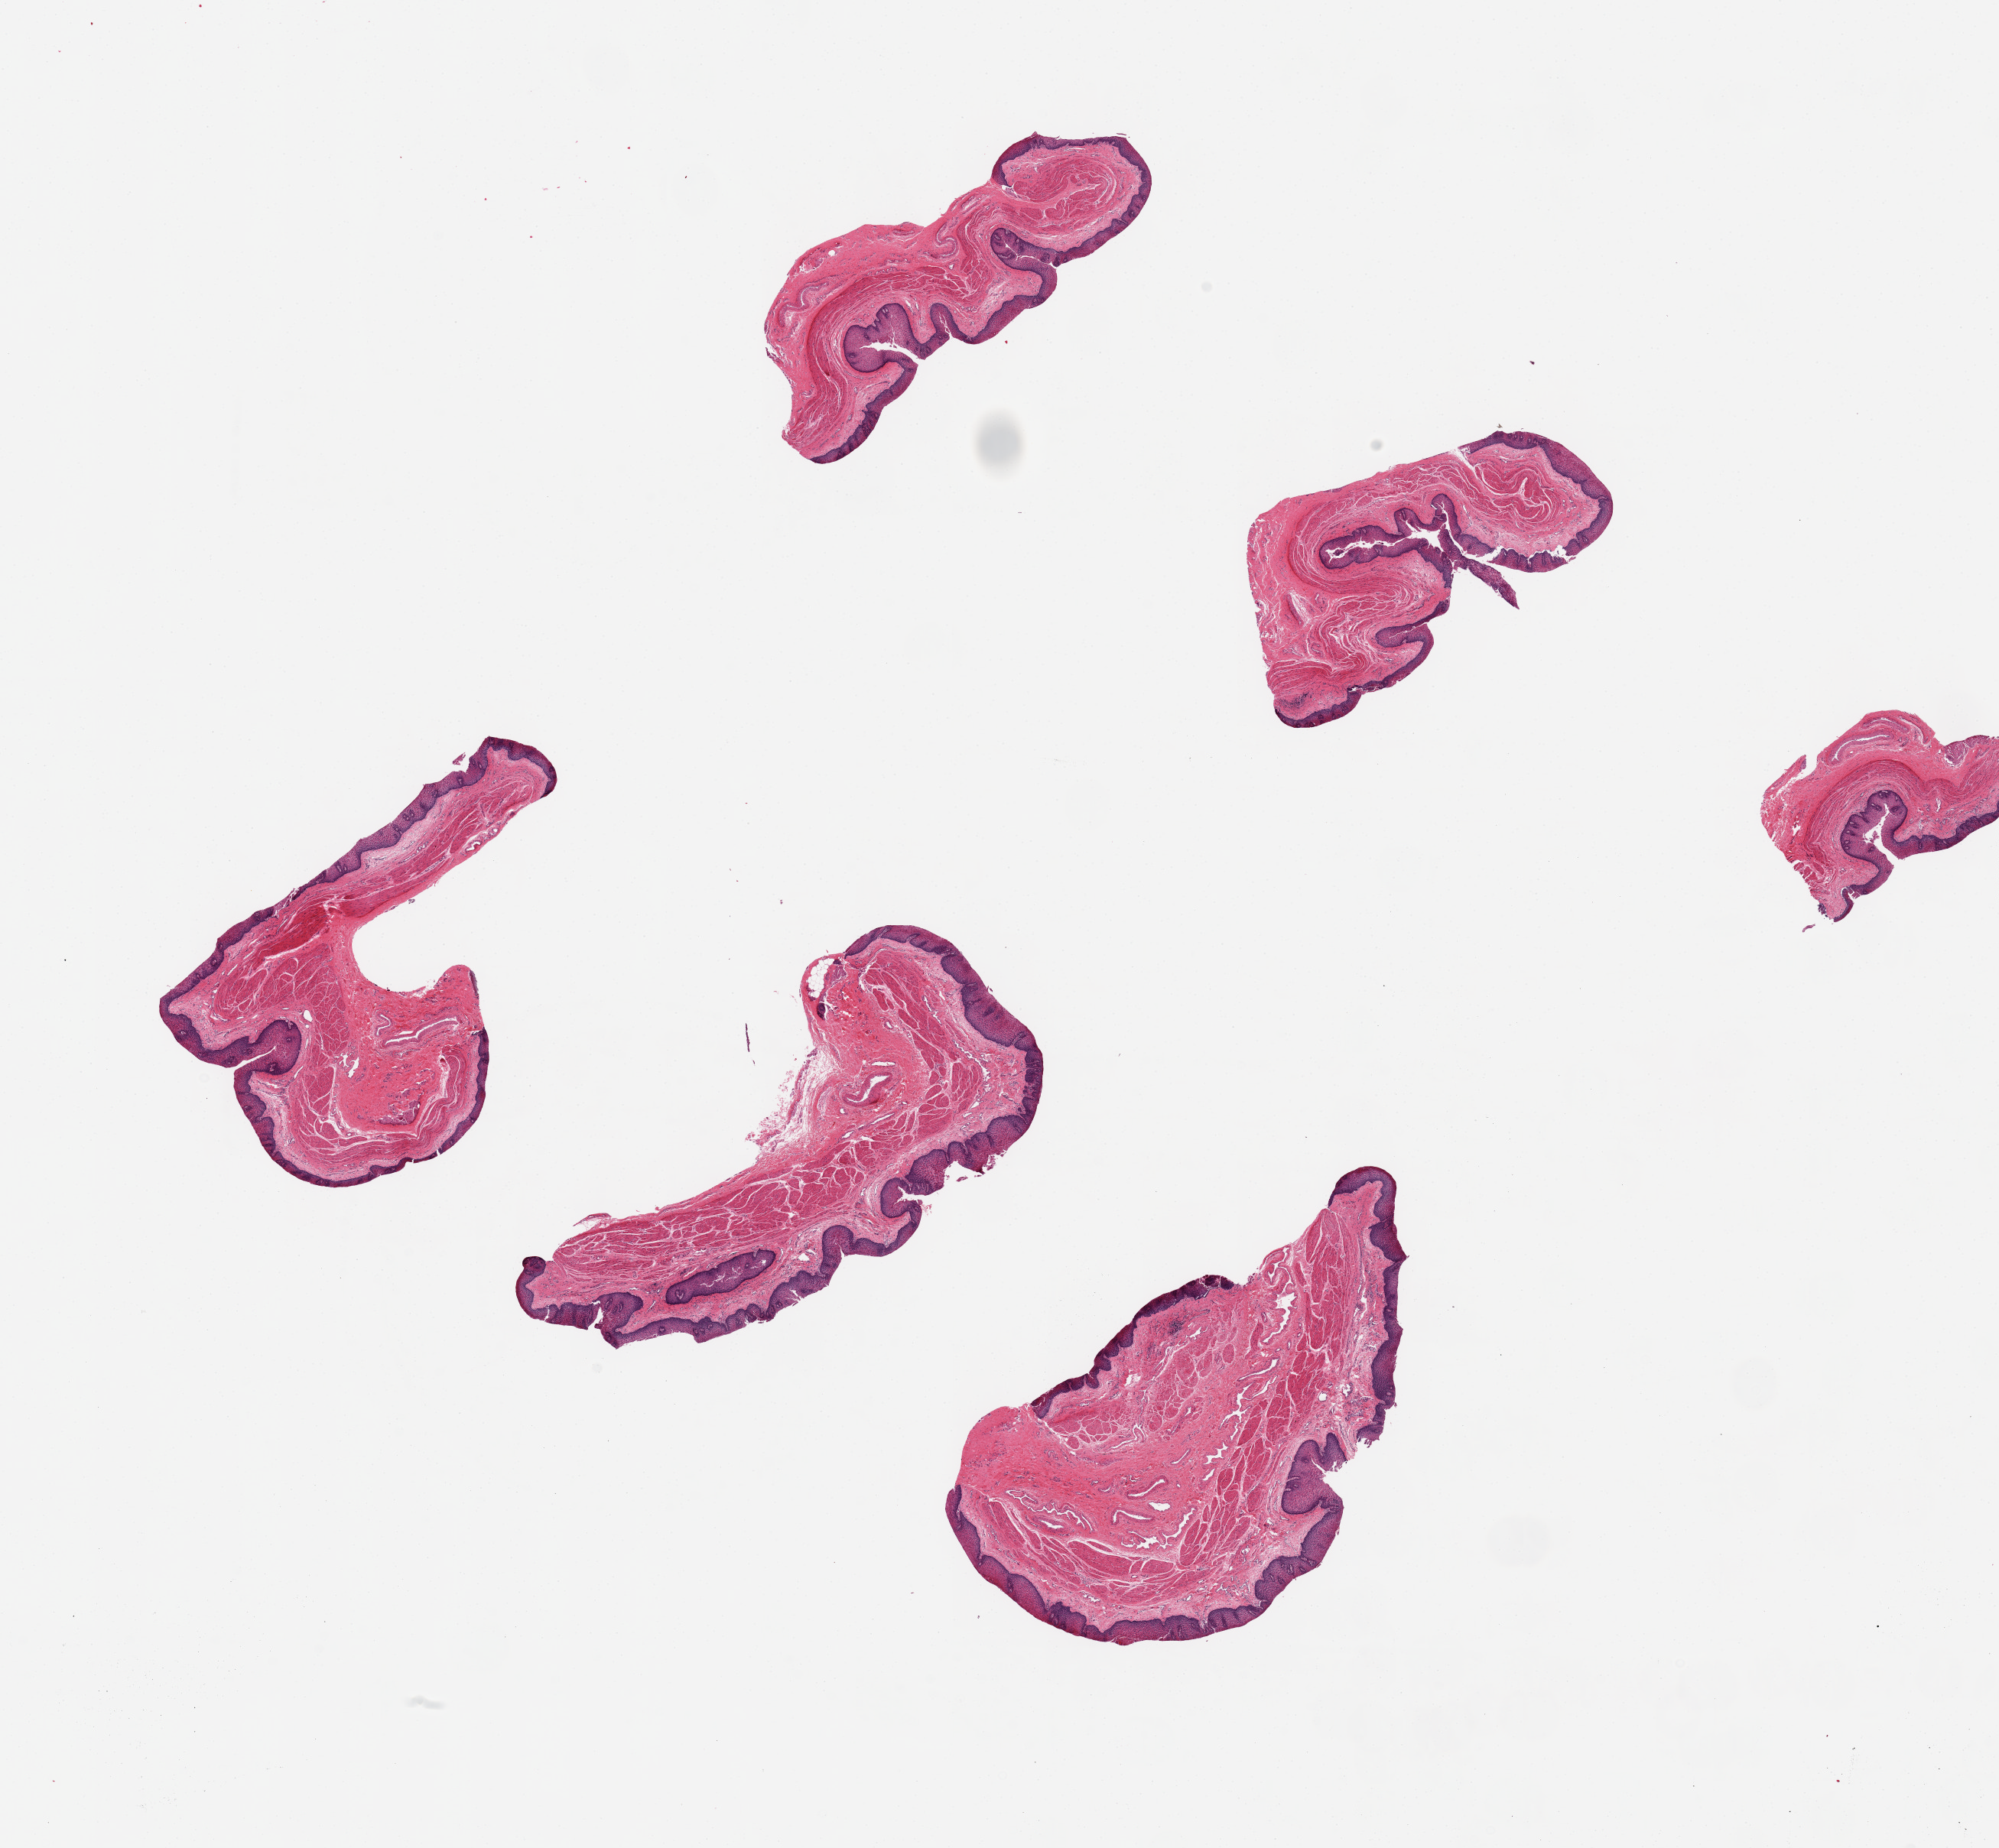
Haematoxylin and eosin whole-slide image, brightfield — whole scanned area (about 20.7 x 19.1 mm, slide scanned at 20x) shown as a low-resolution overview; PAXgene-fixed, paraffin-embedded tissue; target tissue: esophageal mucous membrane; tissue donor sample. Male donor.
Pathologist's review note for this sample: 6 pieces up to 5.9x3.8 mm; good squamous mucosa.